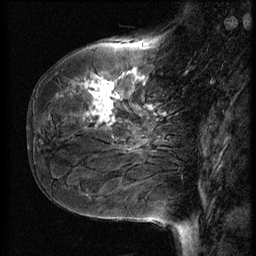
Breast MRI (dynamic contrast-enhanced), one sagittal slice; slice 20 of 56 in the series (ordered by position); 3 images stored at this slice position (order not interpretable as contrast timing); 1.5 T; TE 4.2 ms, TR 9 ms; 2.5 mm slice thickness; 256 × 256 image matrix, field of view 180 × 180 mm. Female patient, age 51 years. From the clinical record (not read from this slice): setting: breast cancer imaged before/during neoadjuvant chemotherapy; receptor status: HR-positive, HER2-negative.
Outlined on this slice (semi-automatically segmented with operator editing):
- analysis volume of interest (the breast-tissue region the enhancement analysis was run in; not a lesion): bounding box <41,58,167,161> (left, top, right, bottom; pixels)
- tumour enhancement mask (voxels above the 140 % enhancement threshold inside the analysis volume of interest): <73,75,153,128>